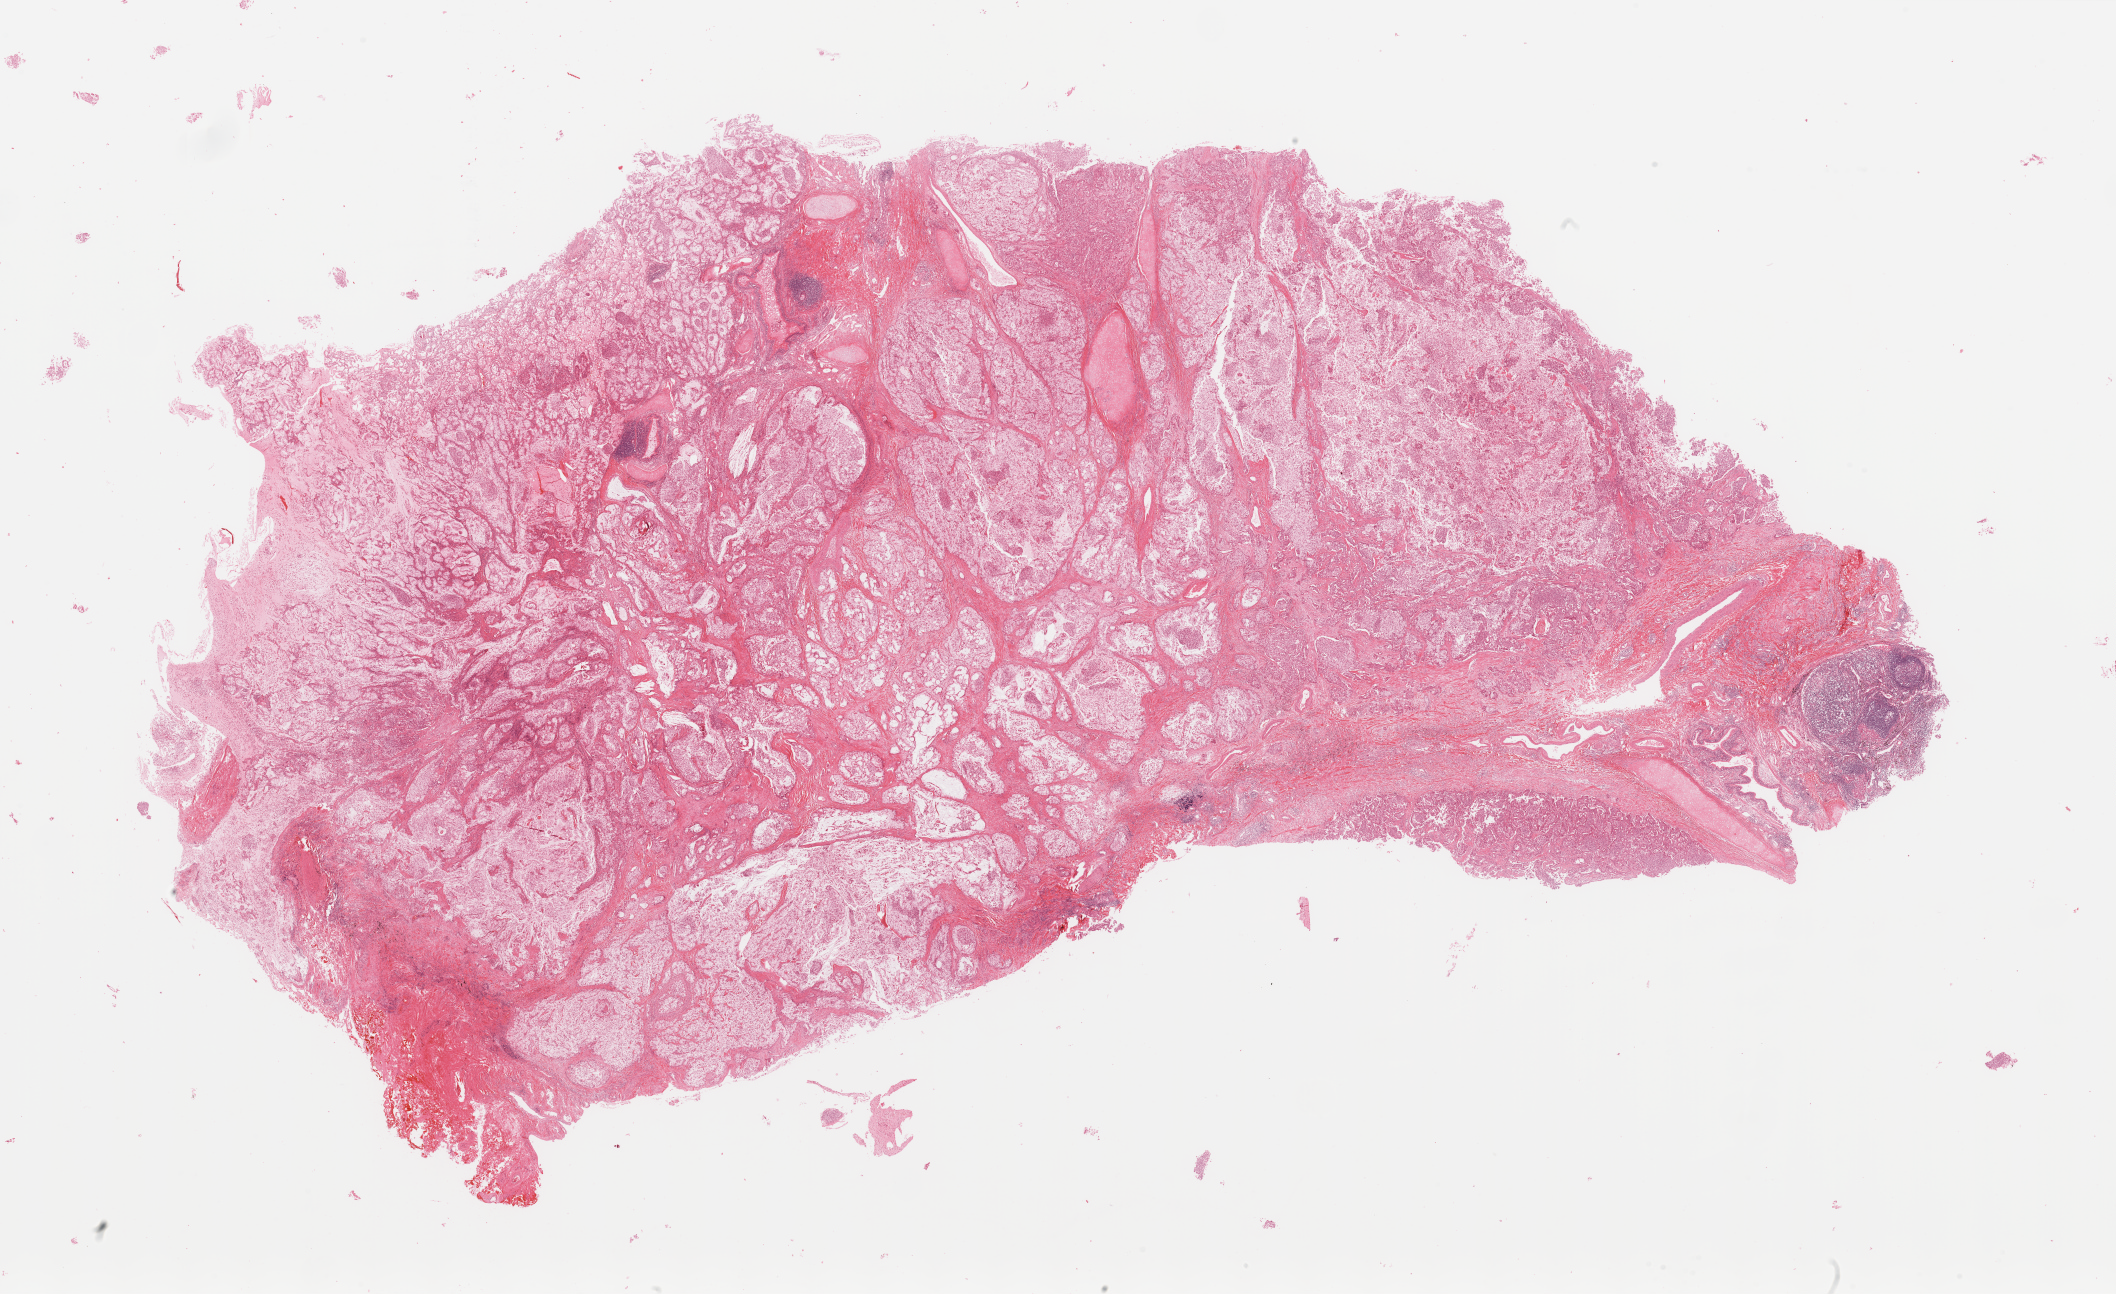
Digitized H&E-stained tissue section (whole slide) — whole scanned area (about 33.5 x 20.5 mm, acquisition: 20x scan) shown as a low-resolution overview; lung, tumour tissue. Female, 25 y/o. Histologic grade: G2 (moderately differentiated).
Diagnosis: Adenocarcinoma, NOS.